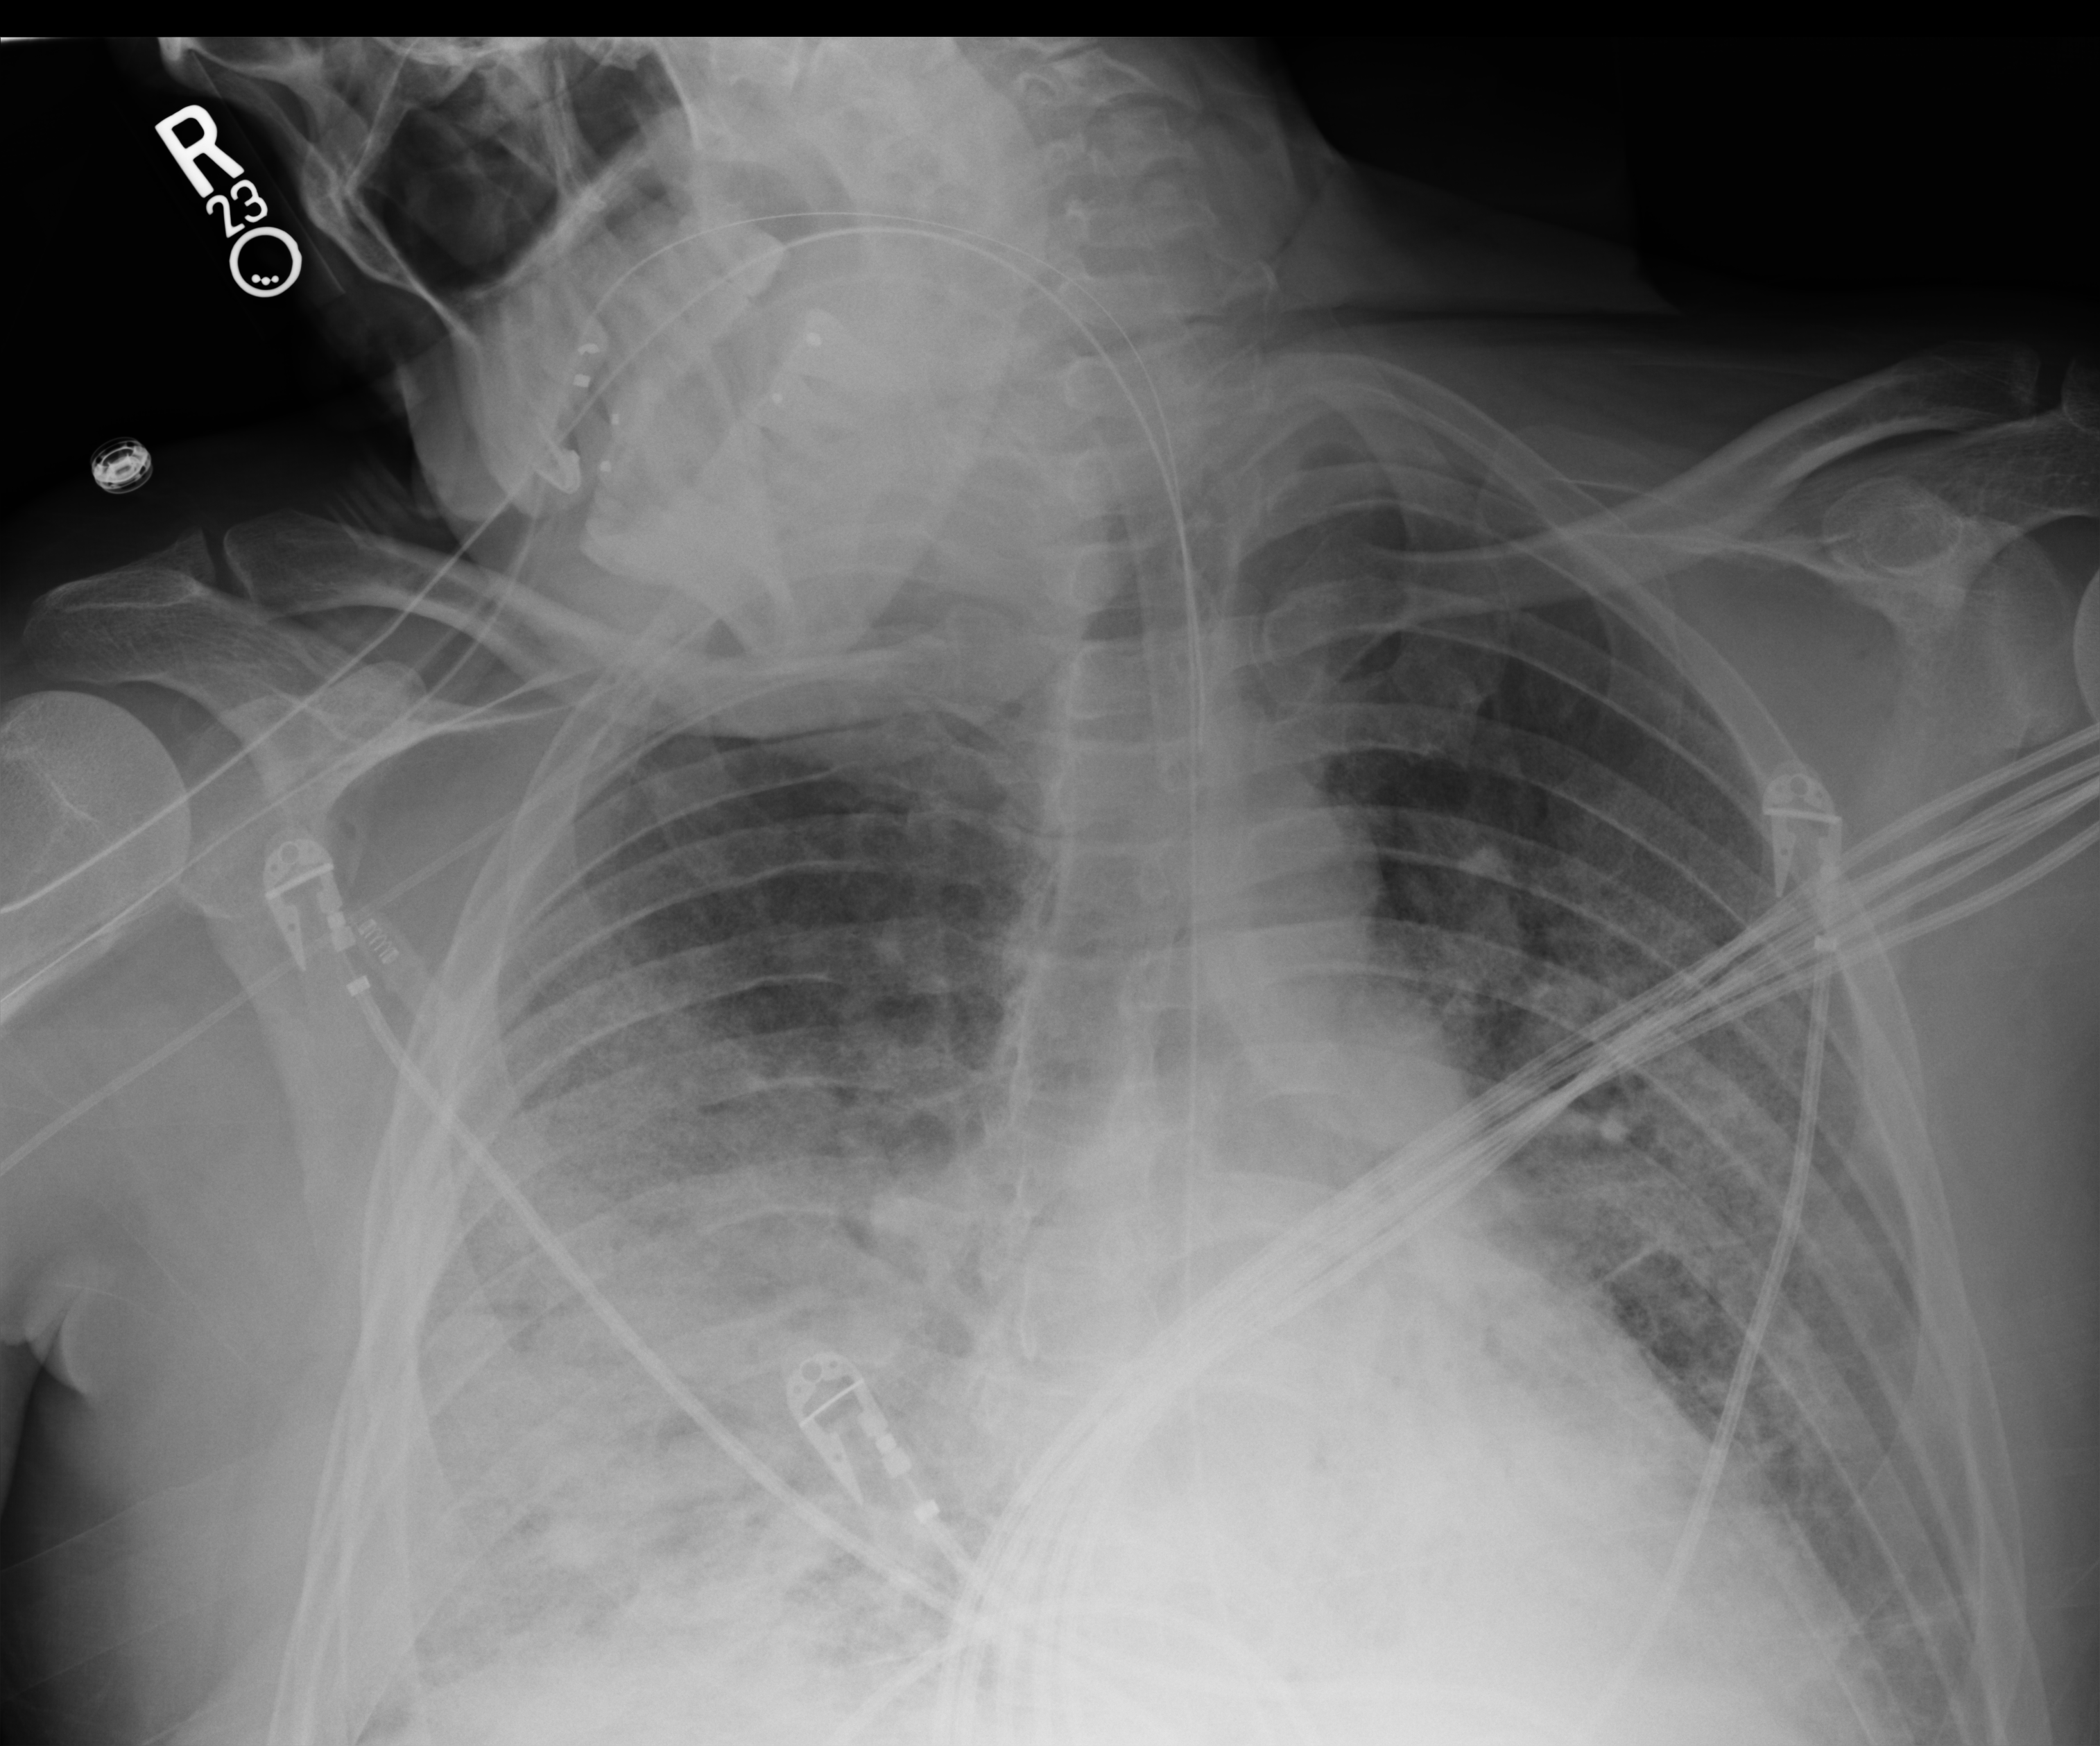
Chest X-ray (portable); anteroposterior (AP) projection. Male patient hospitalised with COVID-19, age 18–59 years.
Hospital-stay facts (about this admission, not read from this image; timing relative to this image not recorded):
- diabetes (admission record): no
- mechanically ventilated during this hospital stay: yes